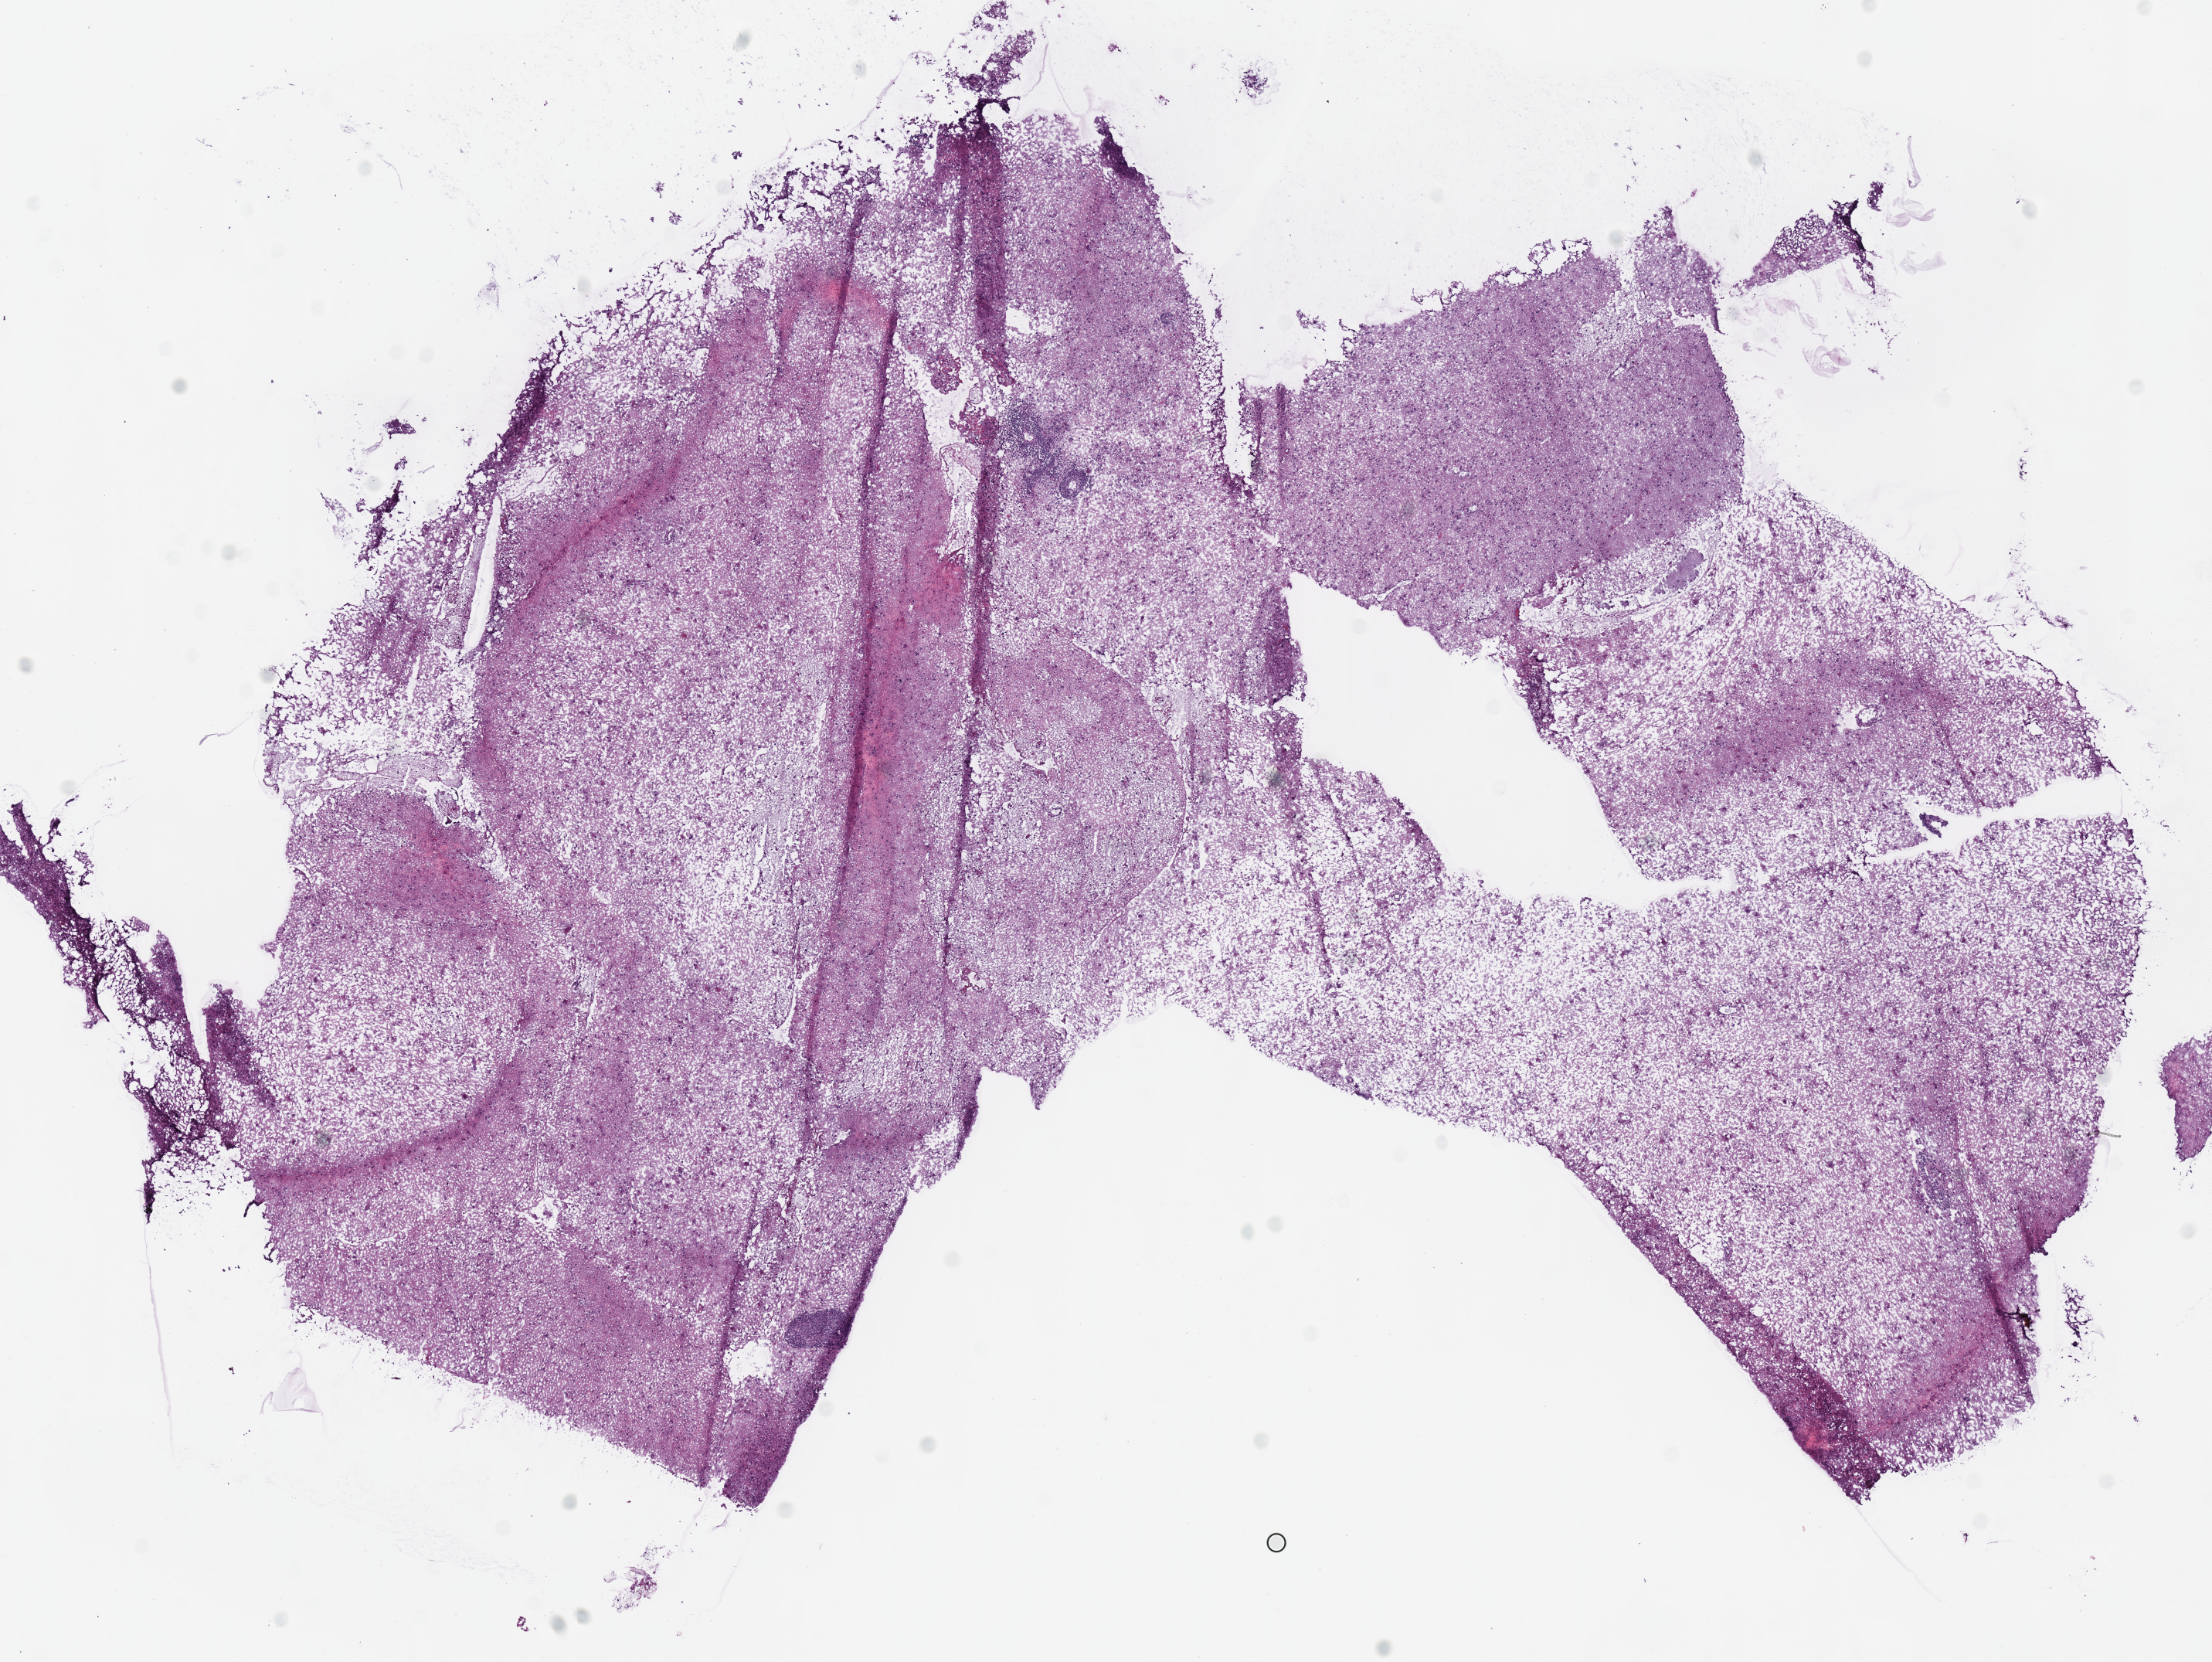
Digitized H&E-stained tissue section (whole slide), a low-resolution overview of the entire scanned area, about 11.3 x 8.5 mm, frozen section from the bottom of the tissue portion, sample: primary tumour, brain. Patient: male, age at initial diagnosis 53 years. Histologic grade: G3 (poorly differentiated). Slide review estimates, as recorded: tumour cells 100%, tumour nuclei 65%, normal cells 0%, stromal cells 0%, necrosis 0%.
Laterality: midline. Histologic diagnosis: Astrocytoma, anaplastic (cerebrum).